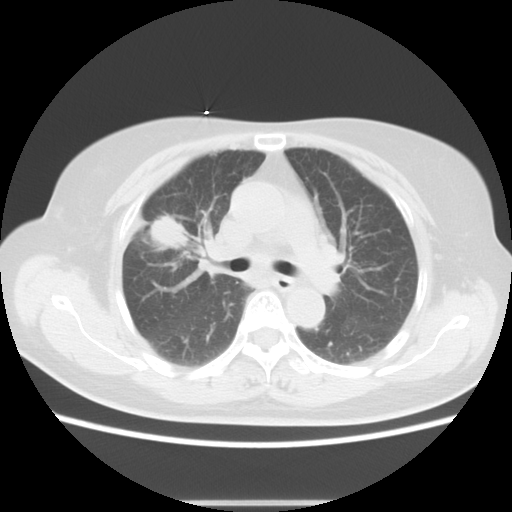
Chest CT, one axial slice; position 7 of 14 along the scan axis; reconstruction kernel STANDARD; 120 kVp; lung window (W 1500 / L -600 HU); 5 mm slice thickness; 512 × 512 image matrix, field of view 350 × 350 mm. Female patient, age 57 years. From the clinical record (not read from this slice): clinical TNM (as recorded): T1c N1 M0.
Annotated regions visible in this slice (rectangle marked by the reading radiologist):
- lung tumour (recorded histology: adenocarcinoma): bounding box [x1, y1, x2, y2] px = [148, 215, 192, 248]